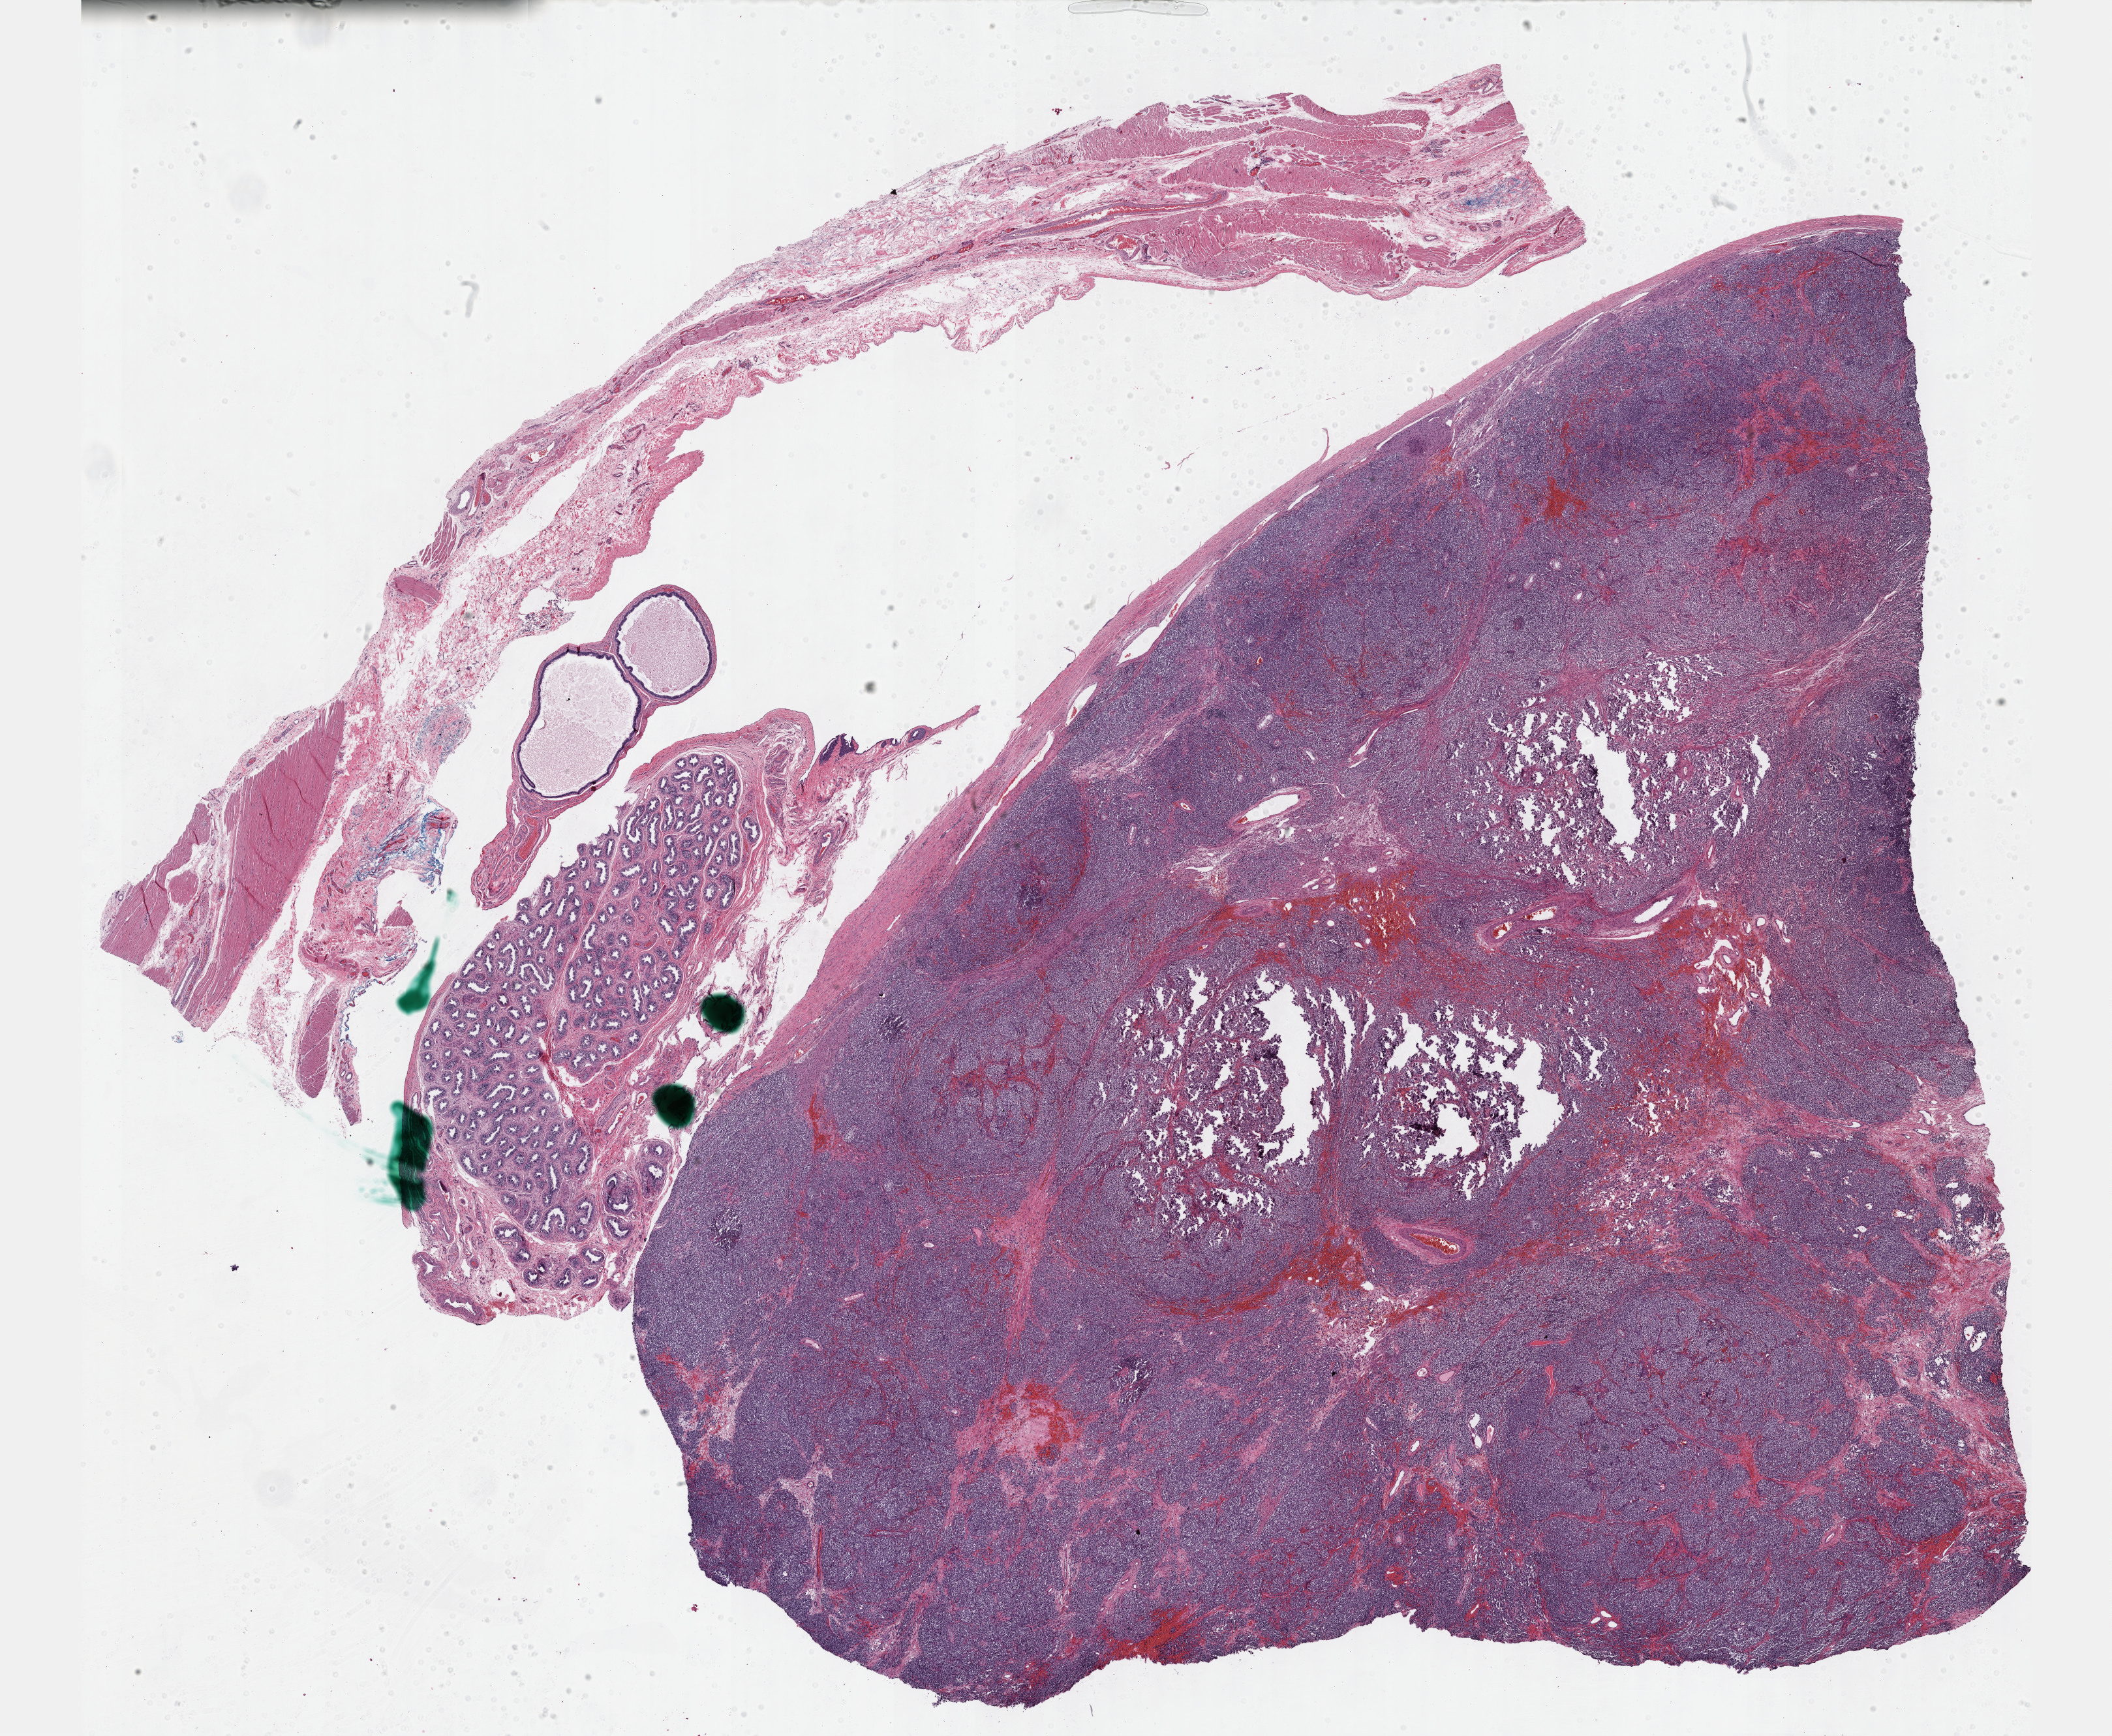
H&E-stained whole-slide image, a low-resolution overview of the entire scanned area, about 26.2 x 21.5 mm. Formalin-fixed paraffin-embedded (FFPE) diagnostic section. Primary tumour sample from the testis. Male, age 26 years at initial diagnosis.
• pathologic diagnosis: Mixed germ cell tumor
• AJCC pathologic stage: IS (7th edition)